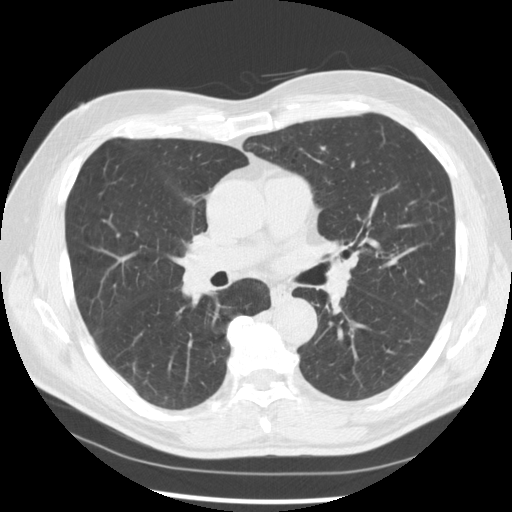
Axial slice from a low-dose chest CT screening exam, baseline screening round, lung window (W 1500 / L -600 HU), 2.5 mm slice thickness, standard (soft-tissue) reconstruction kernel (STANDARD), 120 kVp, slice 158 of 277 in the series, 512 × 512 image matrix. Male participant, aged 67 years at enrolment.
Lesion marked by an expert reader, bounding box (x1, y1, x2, y2) in pixels: (161, 248, 230, 312). Reader record for this screening exam (exam-level; its link to the box is not recorded): non-calcified nodule or mass ≥4 mm, left lower lobe, 15 × 15 mm, spiculated (stellate) margins, soft tissue attenuation. Note: the box lies in the patient's right hemithorax on this image, whereas the reader's record names the left lung; they may be different findings.